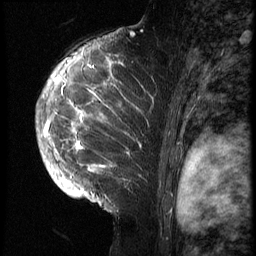
Breast MRI (dynamic contrast-enhanced), one sagittal slice; slice 45 of 70 in the series (ordered by position); 3 images stored at this slice position (order not interpretable as contrast timing); 1.5 T; TE 4.2 ms, TR 9 ms; 256 × 256 image matrix, field of view 180 × 180 mm. Female patient, age 28 years. Case-level facts recorded for this patient, not image findings: setting: breast cancer imaged before/during neoadjuvant chemotherapy.
Structures marked on this image (semi-automatic segmentation, software-assisted and operator-edited):
- analysis volume of interest (the breast-tissue region the enhancement analysis was run in; not a lesion): bounding box (x1, y1, x2, y2) in pixels: (43, 42, 158, 215)
- tumour enhancement mask (voxels above the 140 % enhancement threshold inside the analysis volume of interest): (45, 57, 115, 196)